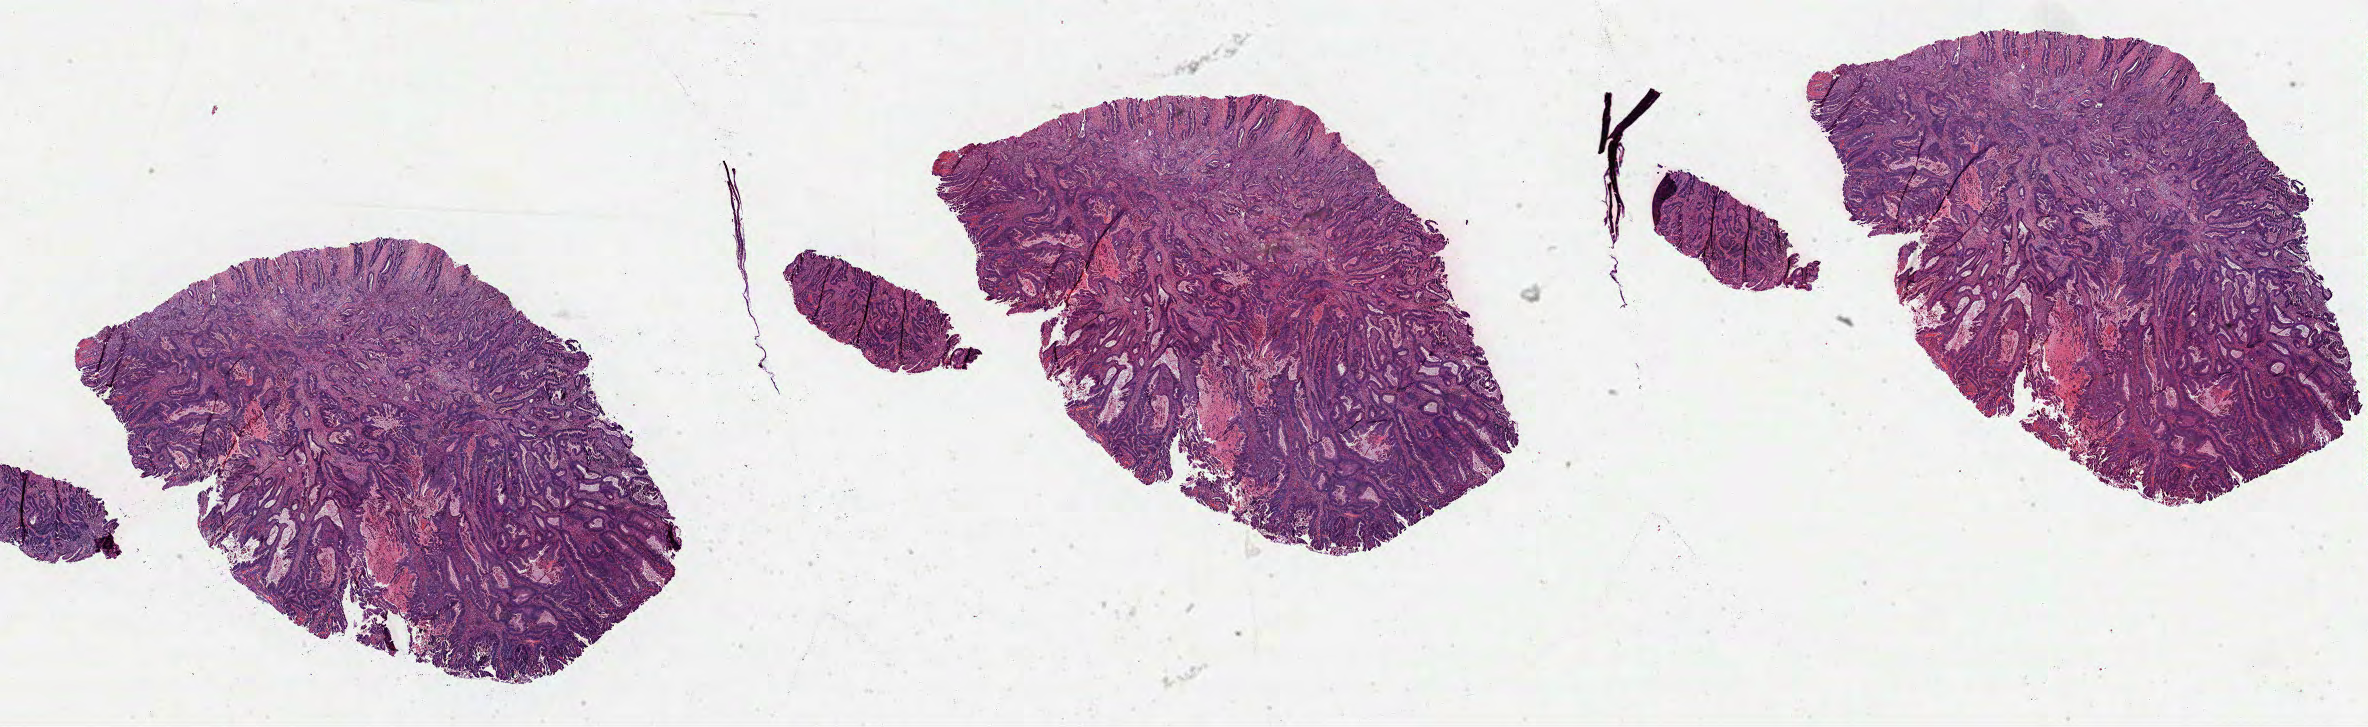
Digitized Hematoxylin and eosin (H&E) stained tissue section (whole slide), low-resolution overview of the scanned area, about 38.2 x 11.7 mm (slide scanned at 40x); FFPE section; colon, primary tumour sample. Female, age 53 years at initial diagnosis.
AJCC pathologic stage: IIIC. Pathologic diagnosis: Adenocarcinoma, NOS (sigmoid colon). Lymph nodes positive (case pathology): 5 of 24 examined.